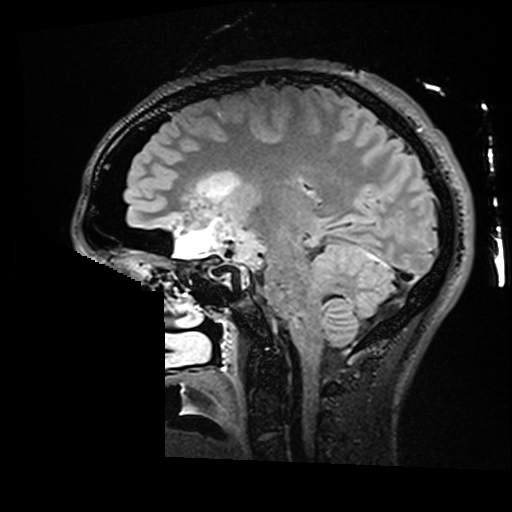
Brain MRI from a brain-tumour surgery series, one sagittal slice. Position 98 of 176 along the scan axis. T2 FLAIR. 1 mm slice thickness. 512 × 512 image matrix. From the clinical record (not read from this slice): histopathology: Astrocytoma; WHO grade: 2; IDH mutation: yes; tumour location: Right Insular.
Structures marked on this image (outlined manually by an expert reader):
- residual tumour: bounding box <198,172,241,200> (left, top, right, bottom; pixels)